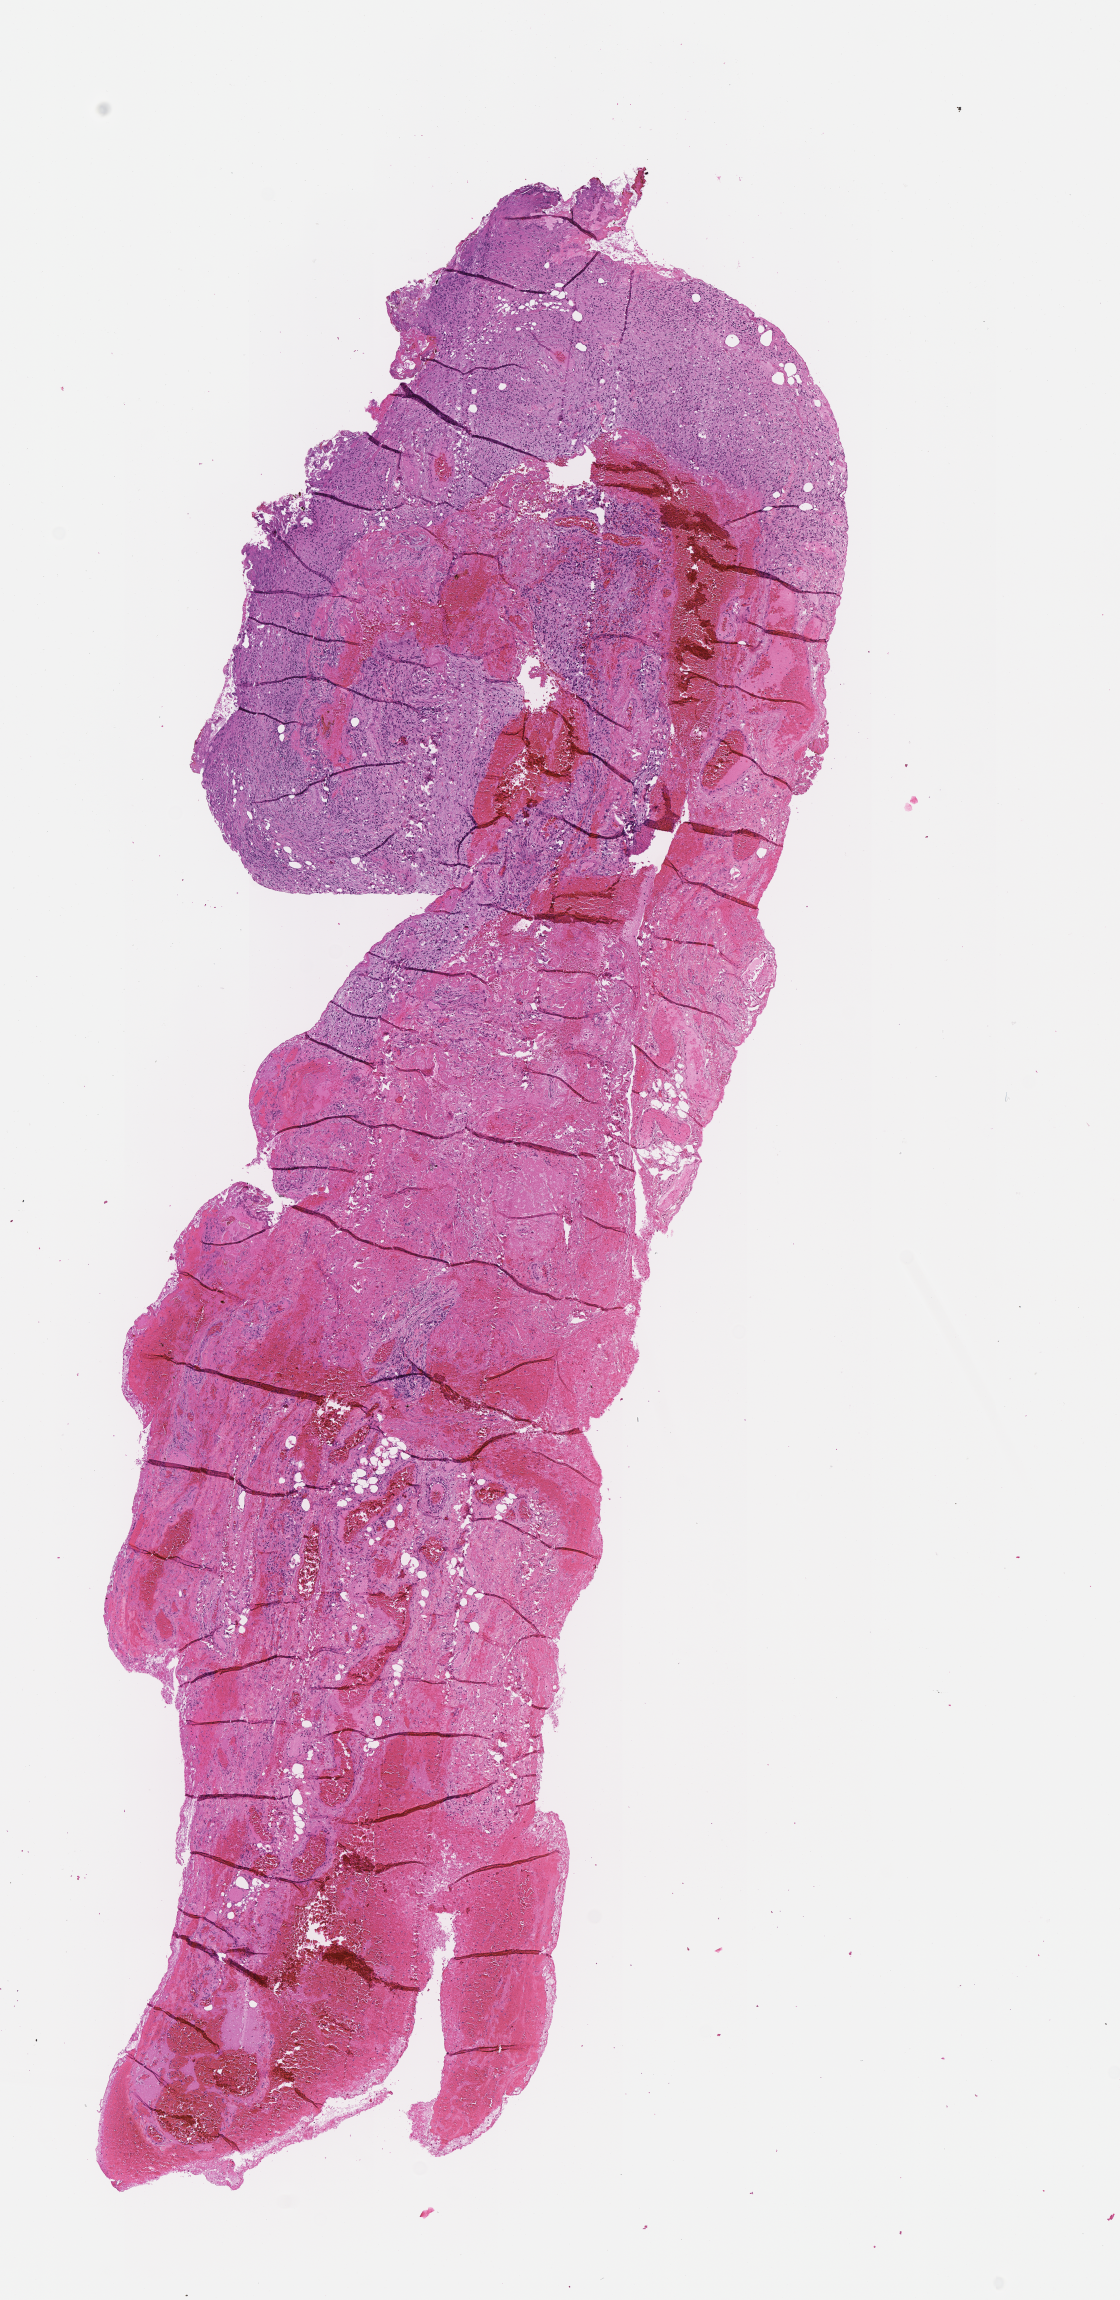
Digitized hematoxylin and eosin (H&E)-stained section of tumor tissue, shown as a low-resolution overview of the whole scanned area (about 4.5 x 9.3 mm). Formalin-fixed paraffin-embedded section. Male patient, age at diagnosis 2.7 years.
Stage (as recorded): 1. Diagnosis: rhabdomyosarcoma; histological classification: botryoid. Metastatic status at presentation (as recorded): non-metastatic.